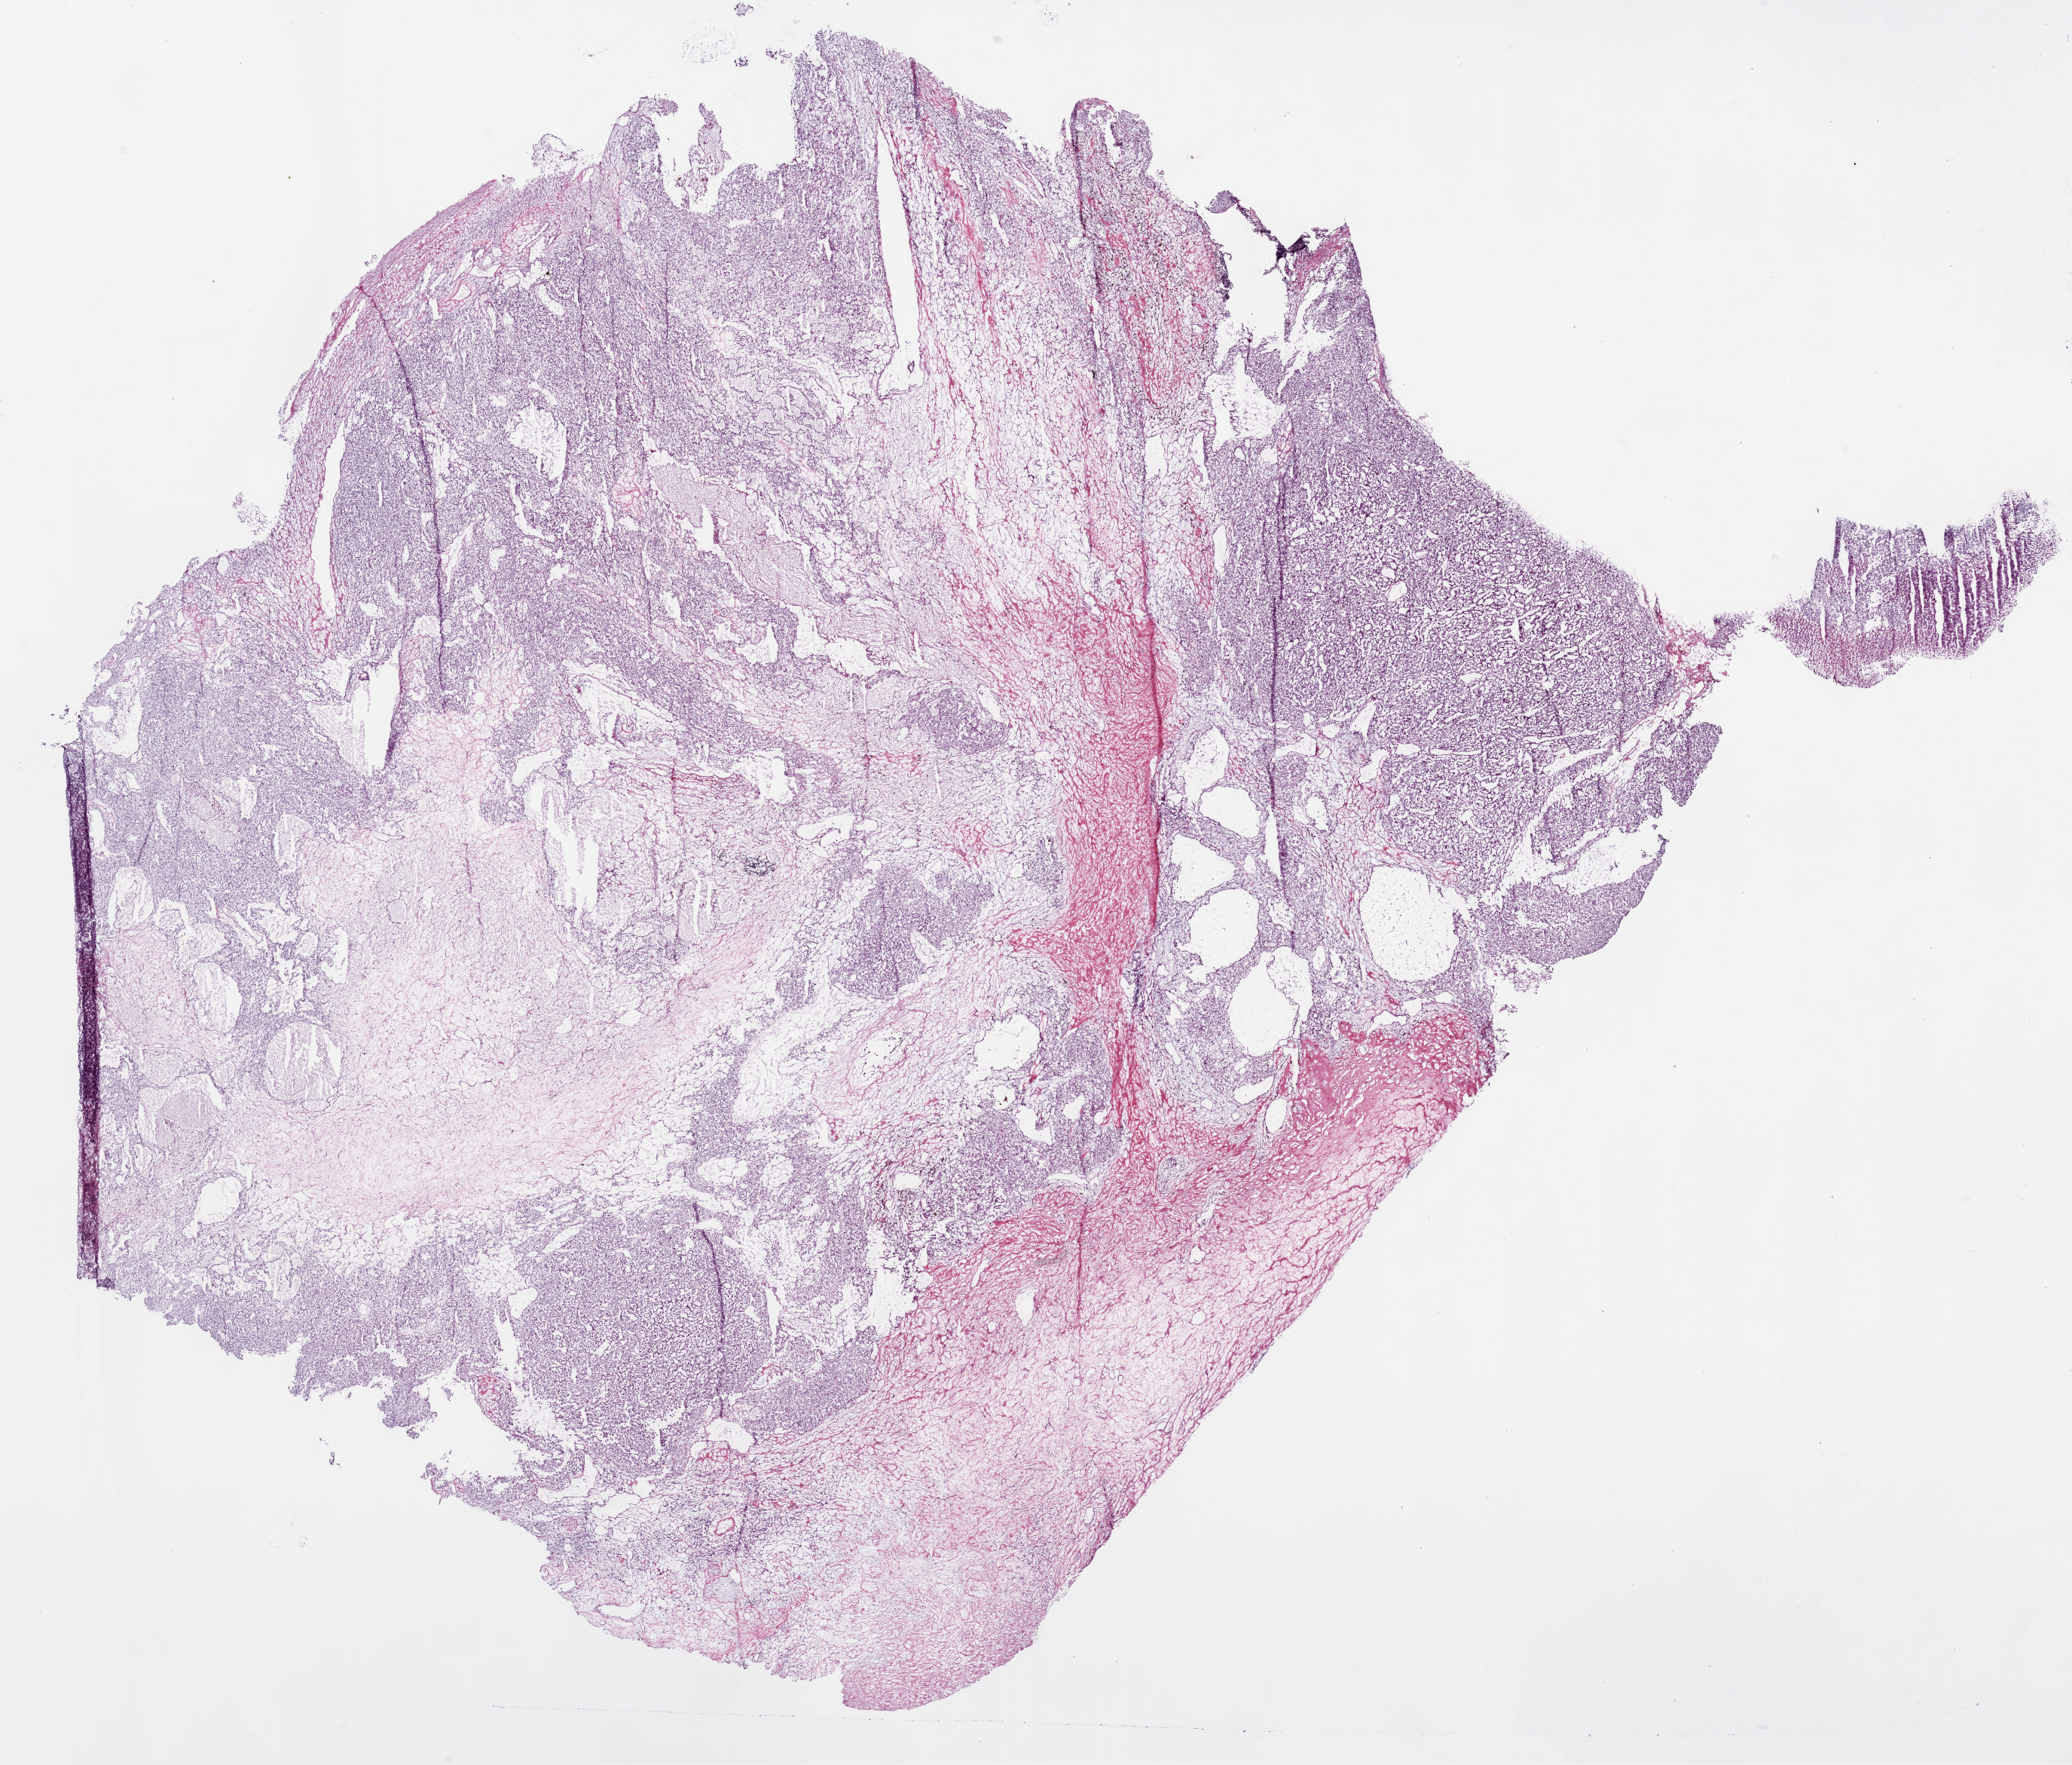
Digitized H&E-stained tissue section (whole slide), whole scanned area (about 22.1 x 18.8 mm, slide scanned at 20x) shown as a low-resolution overview. Frozen section from the bottom of the tissue portion. Primary tumour sample from the kidney. Male, age 44 years at initial diagnosis. Slide review estimates, as recorded: tumour cells 47%, tumour nuclei 80%.
Pathologic diagnosis: Clear cell adenocarcinoma, NOS.